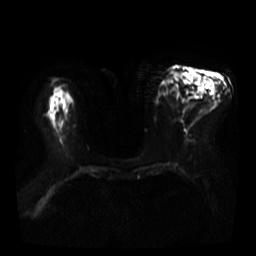
Breast MRI, one axial slice; position 17 of 40 along the scan axis; diffusion-weighted series; image 2 of 4 stored at this slice position (different b-values; order by instance number); 3 T; 5 mm slice thickness; 256 × 256 image matrix, field of view 360 × 360 mm. Female patient.
Annotated regions visible in this slice (manually delineated by an expert):
- tumour on diffusion-weighted imaging: box from (x=193, y=78) to (x=199, y=85) px